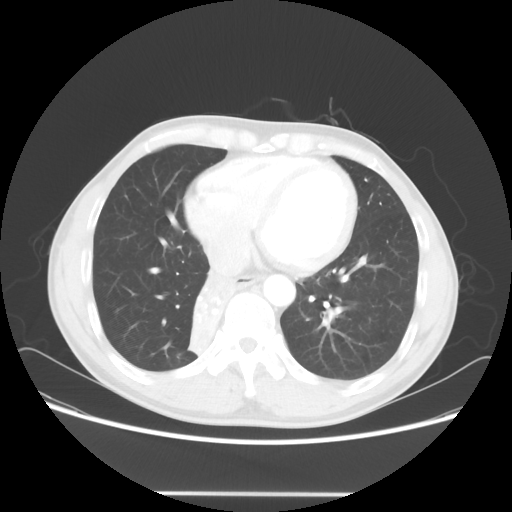
Chest CT, one axial slice. Slice 21 of 62 in the series (ordered by position). Reconstruction kernel STANDARD. 120 kVp. Lung window (W 1500 / L -600 HU). 5 mm slice thickness. 512 × 512 image matrix, field of view 393 × 393 mm. Patient: male, 47 years. Case-level facts recorded for this patient, not image findings: clinical TNM (as recorded): T2 N0 M0; histopathological grade: G2.
Structures marked on this image (bounding box drawn by a radiologist):
- lung tumour (recorded histology: squamous cell carcinoma): box from (x=189, y=277) to (x=227, y=366) px